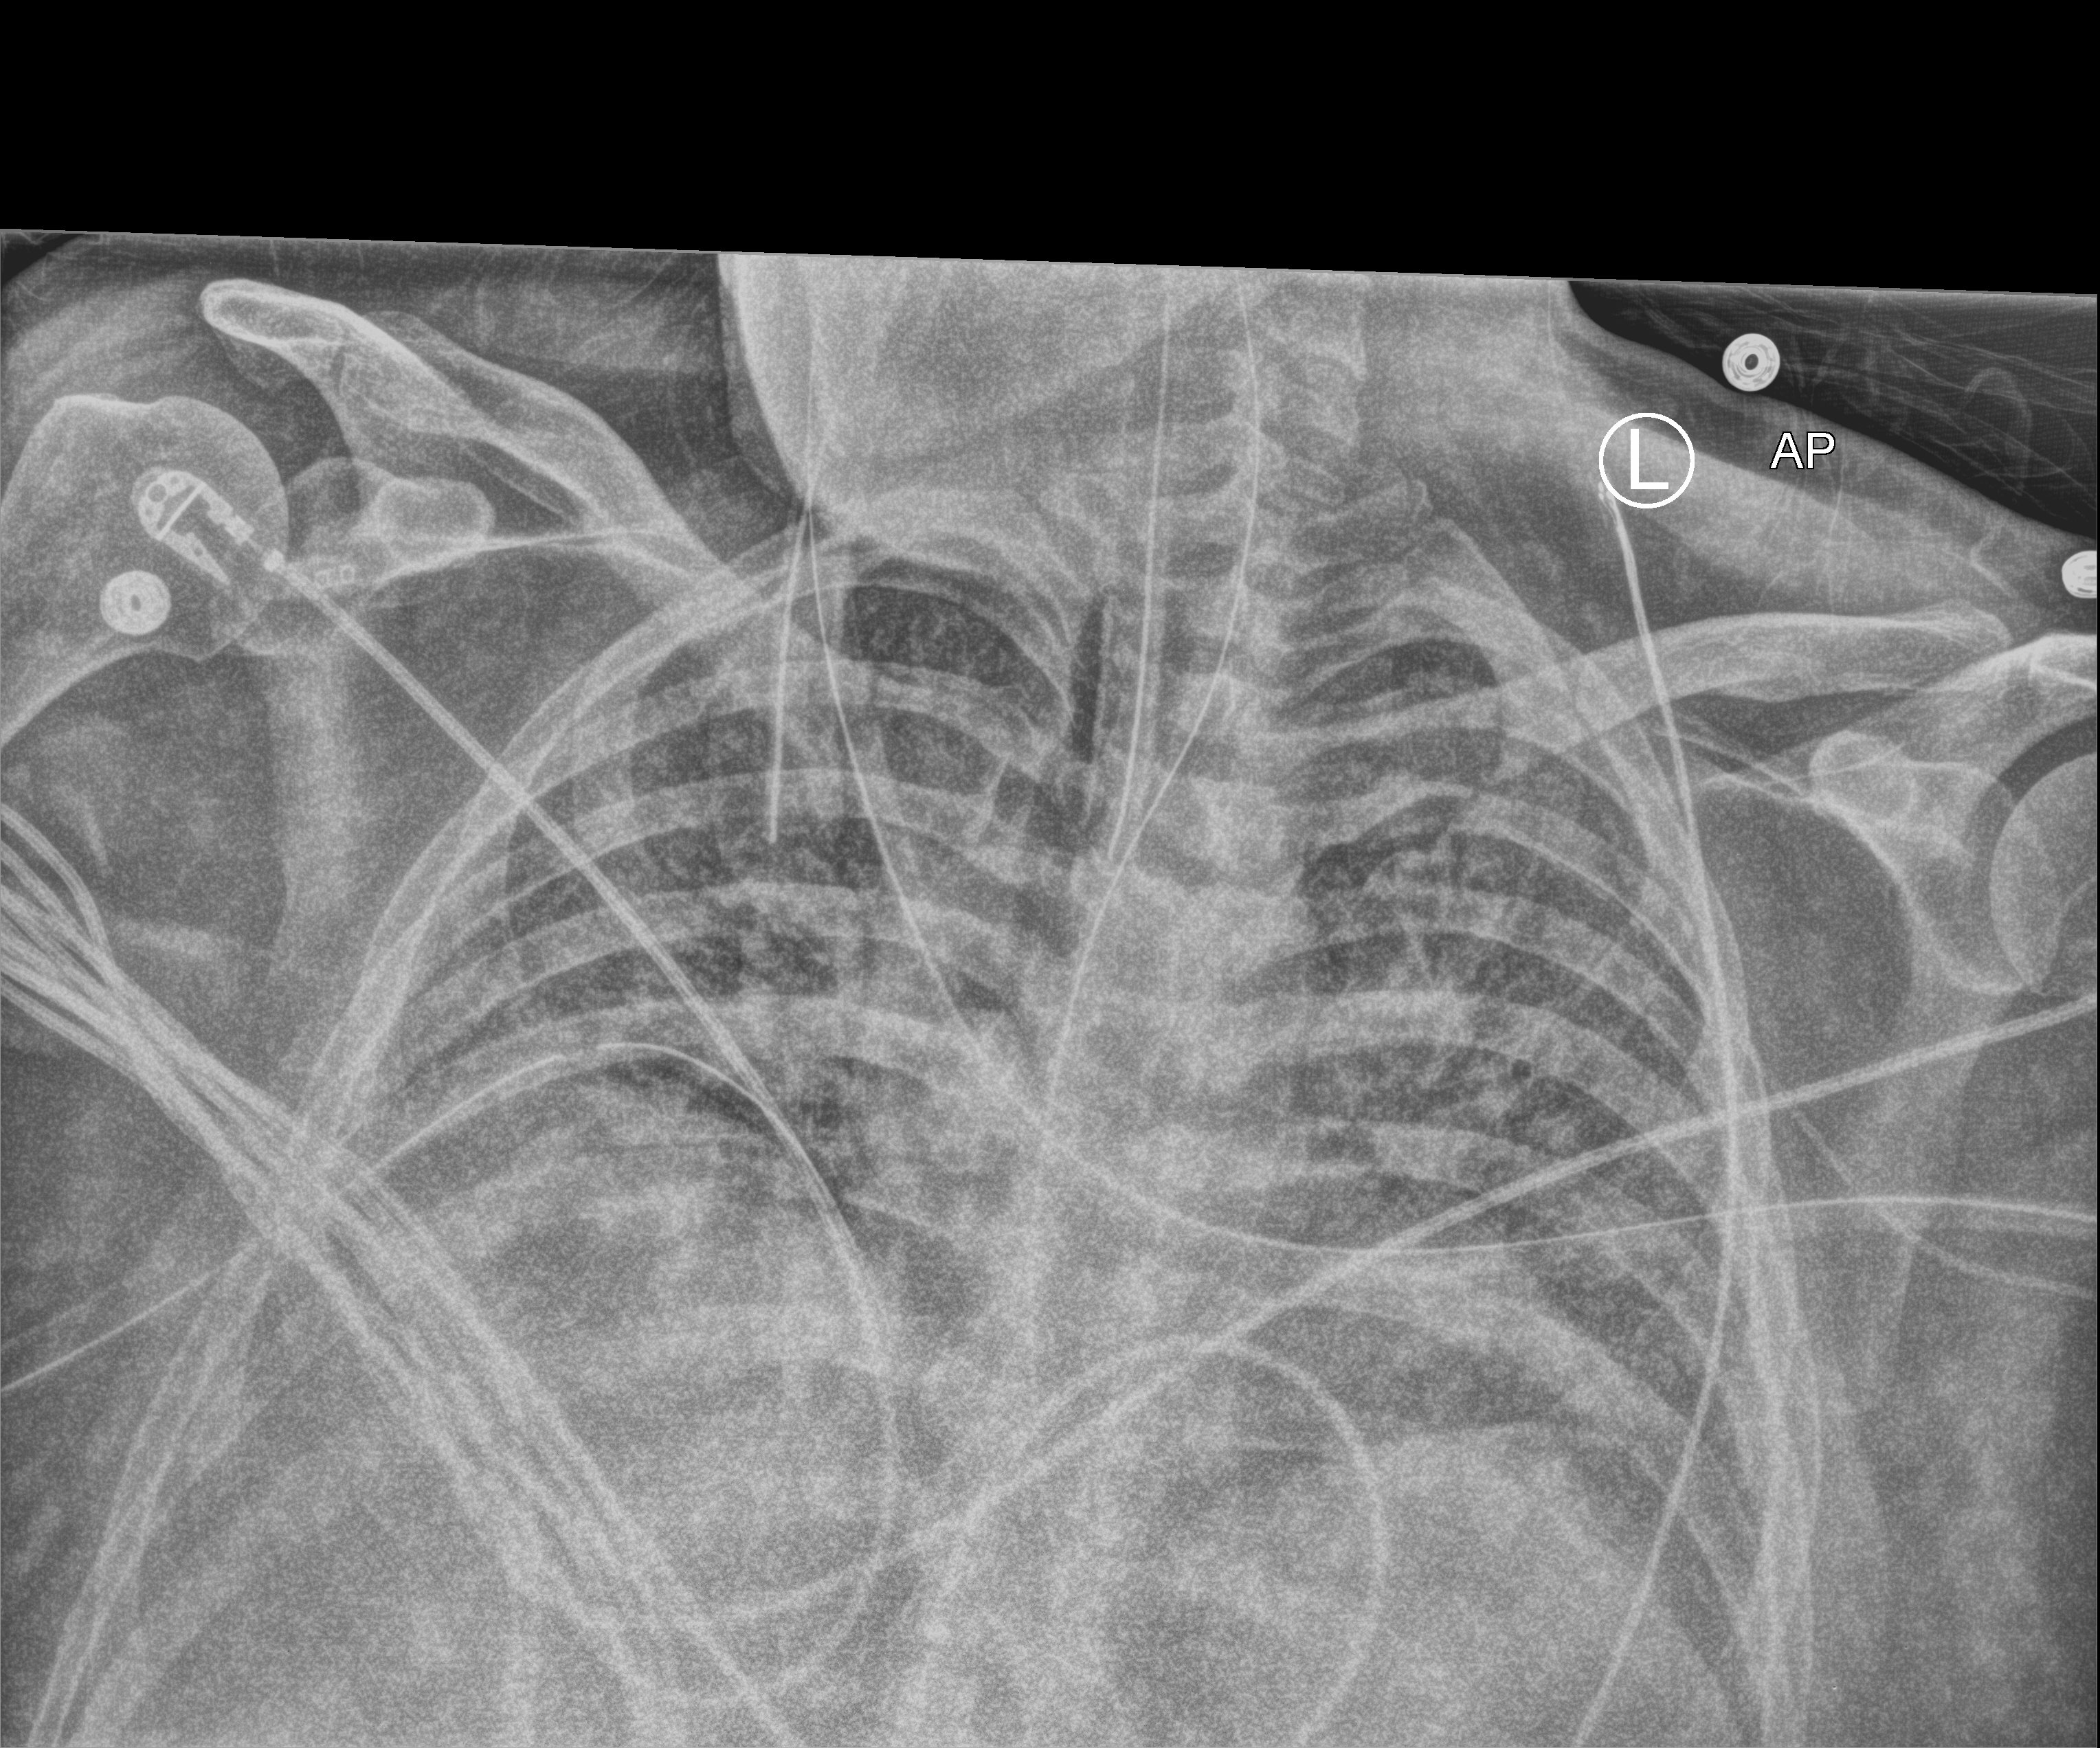
Bedside chest radiograph (computed radiography); anteroposterior (AP) projection. Male patient hospitalised with COVID-19, age 18–59 years.
Admission-level facts for this patient (not findings on this image; timing relative to this image not recorded): hypertension (admission record): yes; mechanically ventilated during this hospital stay: yes; admitted to intensive care during this hospital stay: yes.